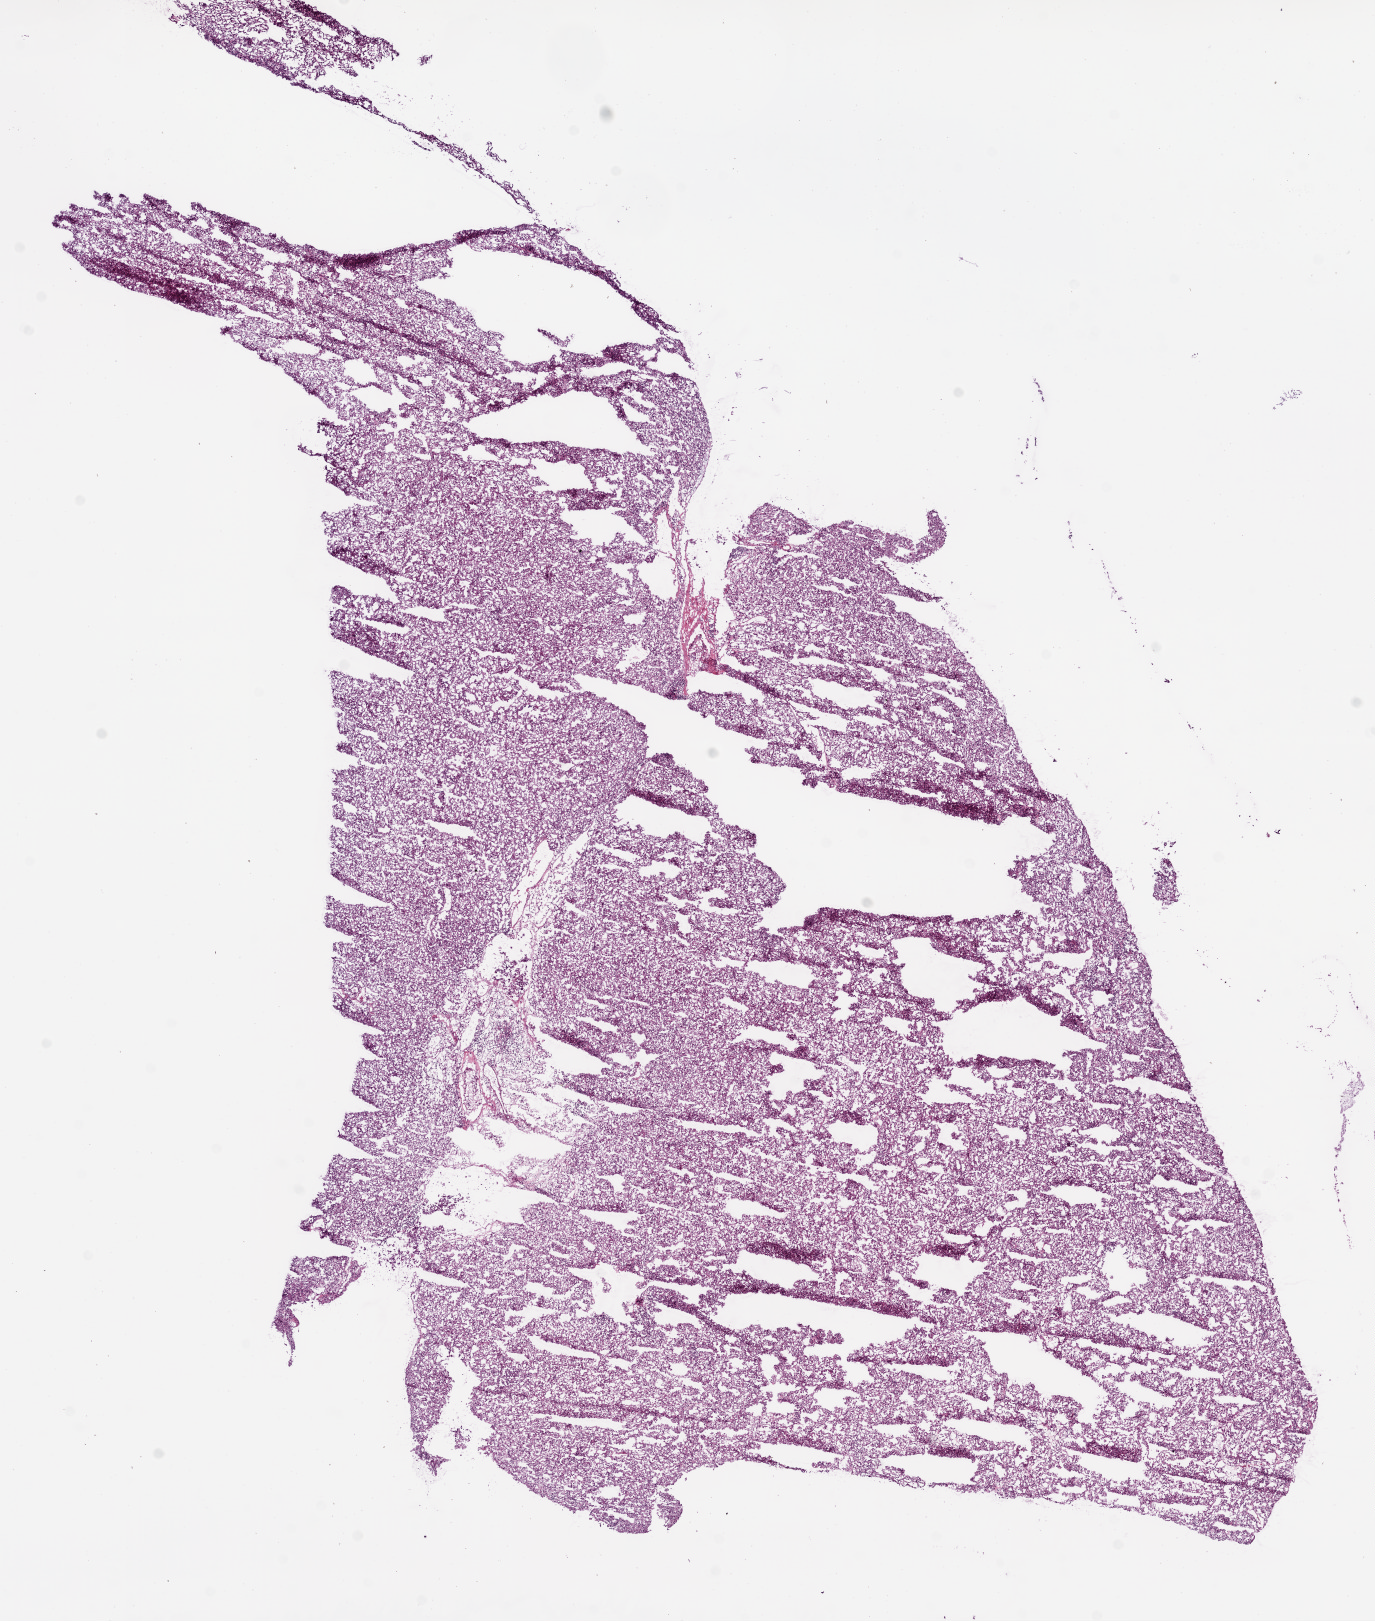
Digitized Hematoxylin and eosin (H&E) stained tissue section (whole slide) — a low-resolution overview of the entire scanned area, about 11.0 x 13.0 mm (slide scanned at 20x). Frozen section. Sample: primary tumour, kidney. Male patient; age at initial diagnosis 60 years. Histologic grade: G3 (poorly differentiated). Pathologist review of this section (percent, as recorded): tumour cells 95%, tumour nuclei 90%, normal cells 0%, stromal cells 5%, necrosis 0%.
TNM: T3a NX M1. Histologic diagnosis: Clear cell adenocarcinoma, NOS. AJCC pathologic stage: IV.